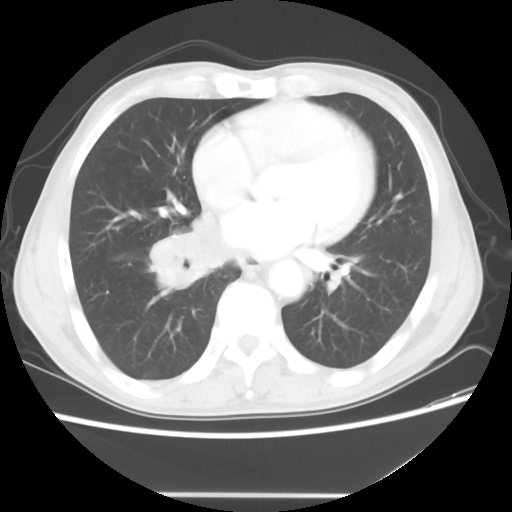
Chest CT, one axial slice. Slice 22 of 56 in the series (ordered by position). Reconstruction kernel STANDARD. 120 kVp. Lung window (W 1500 / L -600 HU). 512 × 512 image matrix, field of view 344 × 344 mm. Patient: male, 65 years. Case-level facts recorded for this patient, not image findings: clinical TNM (as recorded): T1c N3 M0.
Structures marked on this image (rectangle marked by the reading radiologist):
- lung tumour (recorded histology: small cell carcinoma): bounding box [x1, y1, x2, y2] px = [147, 216, 235, 290]